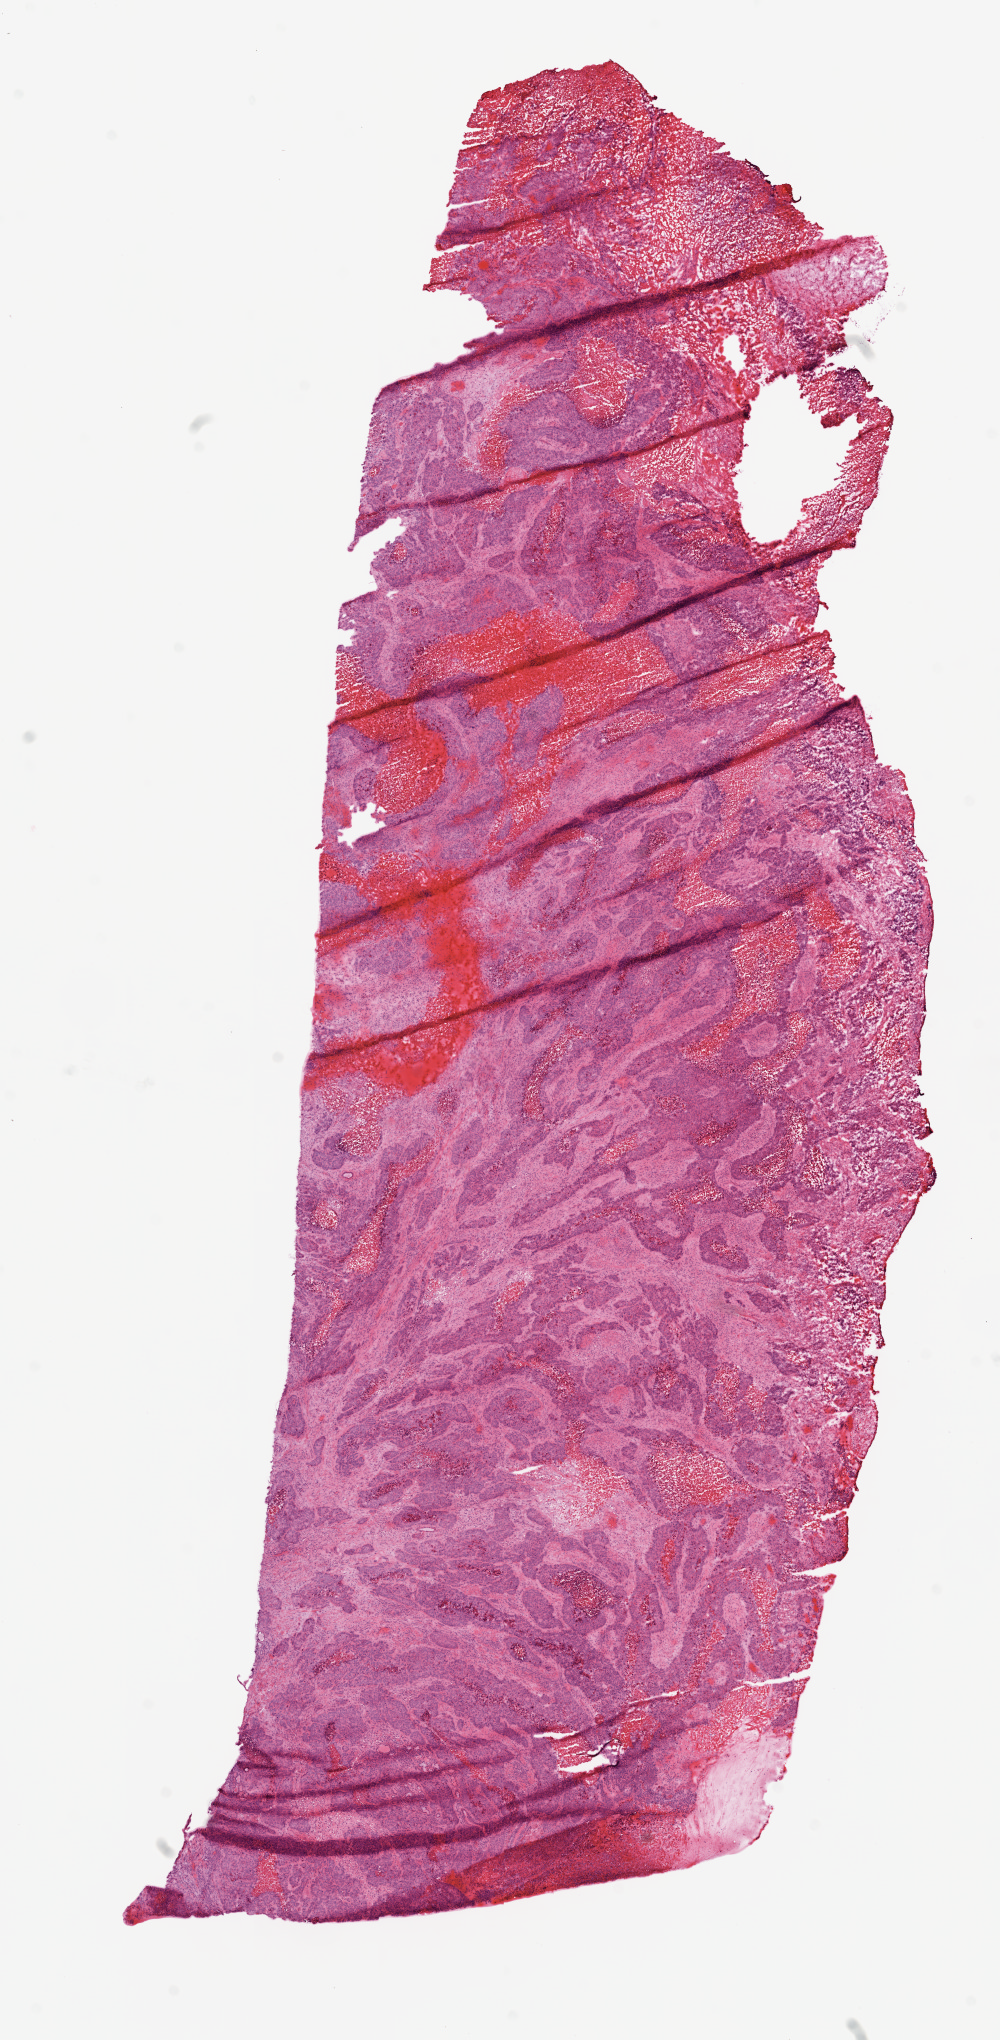
Digitized H&E tissue section (whole slide) — a low-resolution overview of the entire scanned area, about 8.0 x 16.4 mm (from a 20x scan), frozen section, sample: primary tumour, lung. Patient: male, age at initial diagnosis 74 years. Composition of this section per pathologist review: tumour cells 60%, tumour nuclei 80%, normal cells 0%, stromal cells 25%, necrosis 15%. Infiltration values recorded for this section: lymphocyte infiltration 5%, monocyte infiltration 0%, neutrophil infiltration 0%.
- pathologic diagnosis: Squamous cell carcinoma, NOS (upper lobe, lung)
- laterality: right
- AJCC pathologic stage: IIA